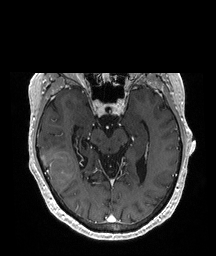
Brain MRI from a brain-tumour surgery series, one axial slice; T1-weighted post-contrast; 216 × 256 image matrix, field of view 216 × 256 mm. Case-level facts recorded for this patient, not image findings: histopathology: Glioblastoma; WHO grade: 4; IDH mutation: no; tumour location: Right Temporal.
Annotated regions visible in this slice (manually delineated by an expert):
- tumour: bounding box [x1, y1, x2, y2] px = [41, 151, 76, 194]